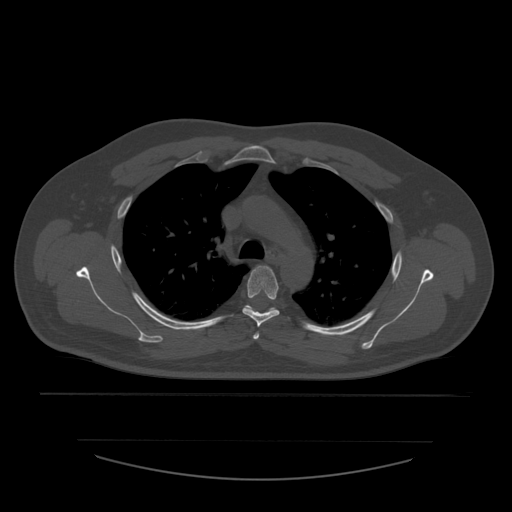
CT including the spine, one axial slice; slice 415 of 532 in the series (ordered by position); 120 kVp; bone window (W 1800 / L 400 HU); 1.25 mm slice thickness; 512 × 512 image matrix, field of view 441 × 441 mm. Patient age 44 years. Case-level facts recorded for this patient, not image findings: primary cancer: soft tissue sarcoma.
Annotated regions visible in this slice (semi-automatically segmented with operator editing):
- T3 vertebra: bounding box <253,327,260,340> (left, top, right, bottom; pixels)
- T4 vertebra: <242,266,280,327>
- T5 vertebra: <245,305,278,313>